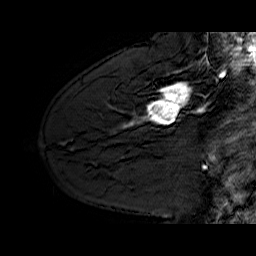
Breast MRI (dynamic contrast-enhanced), one sagittal slice; slice 43 of 60 in the series (ordered by position); dynamic contrast-enhanced series, time point 2 of 6 at this slice position (early post-contrast); 1.5 T; TE 6.4 ms, TR 32.9 ms; 4 mm slice thickness; 256 × 256 image matrix. Female patient. From the clinical record (not read from this slice): setting: breast cancer imaged before/during neoadjuvant chemotherapy; receptor status: HER2-positive.
Structures marked on this image (semi-automatic segmentation, software-assisted and operator-edited):
- analysis volume of interest (the breast-tissue region the enhancement analysis was run in; not a lesion): bounding box (x1, y1, x2, y2) in pixels: (130, 62, 209, 127)
- tumour enhancement mask (voxels above the 100 % enhancement threshold inside the analysis volume of interest): (130, 84, 200, 126)